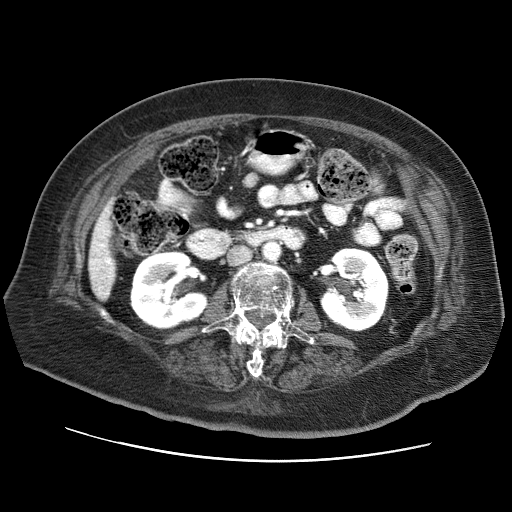
Contrast-enhanced abdominal CT (liver protocol), one axial slice; position 18 of 73 along the scan axis; soft-tissue window (W 400 / L 40 HU); 2.5 mm slice thickness; 512 × 512 image matrix, field of view 380 × 380 mm. From the clinical record (not read from this slice): diagnosis: hepatocellular carcinoma (patient treated with transarterial chemoembolisation; whether this scan precedes or follows treatment is not stated here); TNM stage (as recorded): Stage-I; Child-Pugh class: A.
Annotated regions visible in this slice (semi-automatic segmentation, software-assisted and operator-edited):
- liver parenchyma outside the tumour (the mass and vessels are separate outlines, so this box may not span the whole liver): bounding box (x1, y1, x2, y2) in pixels: (88, 200, 116, 300)
- liver vessels: (92, 230, 111, 264)